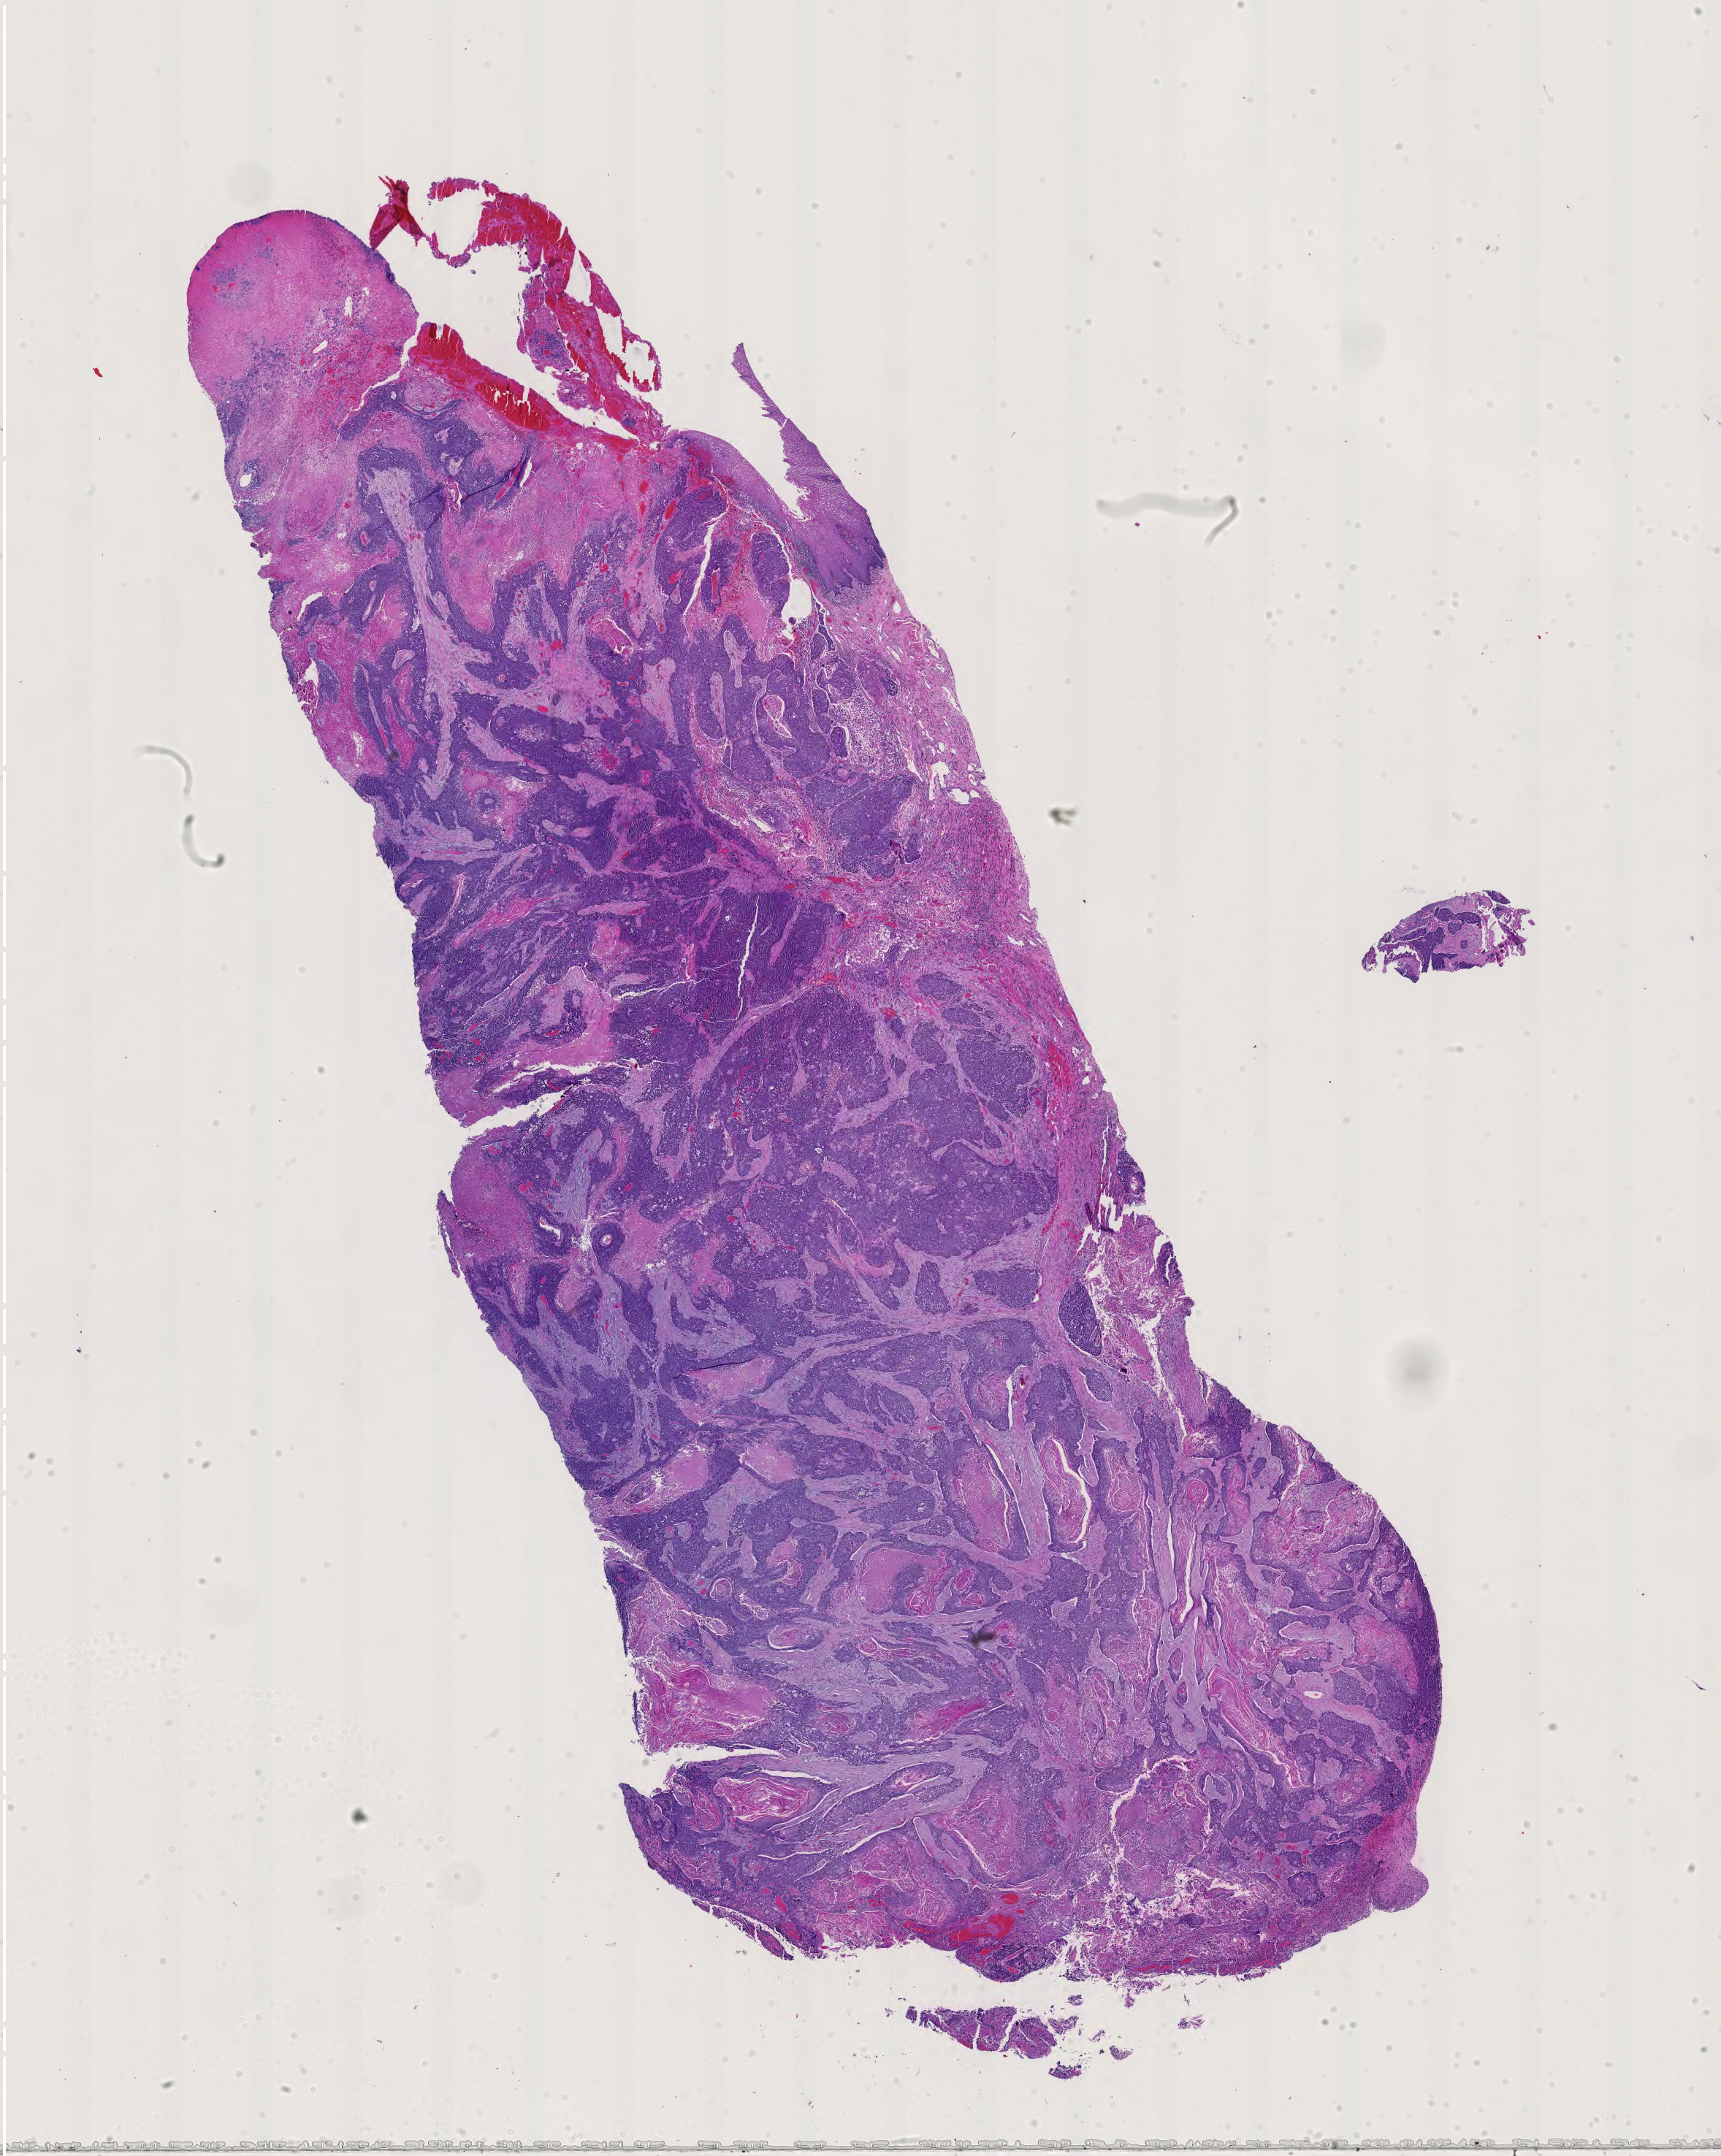
H&E whole-slide image, shown as a low-resolution overview of the whole scanned area (about 17.1 x 21.4 mm, acquisition: 40x scan). Formalin-fixed paraffin-embedded (FFPE) diagnostic section. Sample: primary tumour, head and neck. Patient: male, age at initial diagnosis 66 years. Histologic grade: G2 (moderately differentiated).
Laterality: left. AJCC pathologic stage: IVA. TNM: T4a N0 M0. Diagnosis: Squamous cell carcinoma, NOS (floor of mouth, NOS).